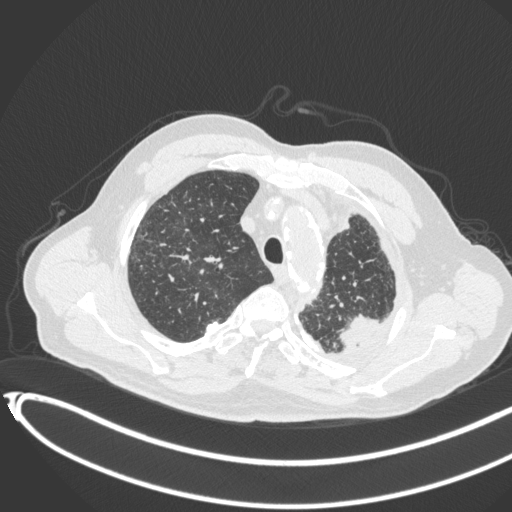
Chest CT, one axial slice; slice 346 of 451 in the series (ordered by position); lung window (W 1500 / L -600 HU); 512 × 512 image matrix, field of view 400 × 400 mm. Patient: male, 78 years. Case-level facts recorded for this patient, not image findings: clinical TNM (as recorded): T1c N0 M1.
Structures marked on this image (rectangle marked by the reading radiologist):
- lung tumour (recorded histology: adenocarcinoma): bounding box (x1, y1, x2, y2) in pixels: (335, 308, 386, 359)